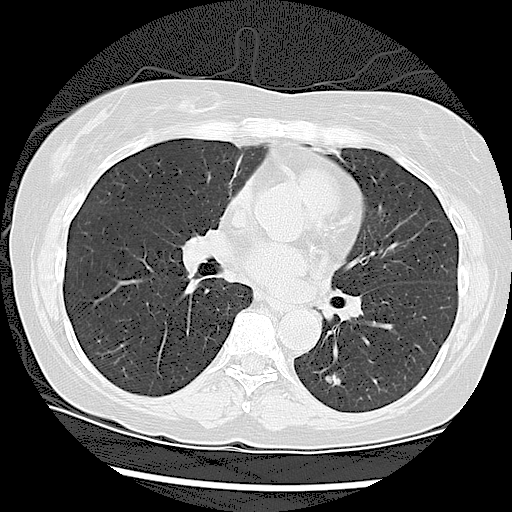
Low-dose screening chest CT, axial slice; second annual screen; lung window (W 1500 / L -600 HU); 2.5 mm slice thickness; slice 57 of 108 in the series; 512 × 512 image matrix. Female, age 61 years at enrolment. Current smoker at enrolment.
Expert-annotated lung lesion, bounding box <303,361,364,406> (left, top, right, bottom; pixels). The screening reader recorded 2 non-calcified nodules or masses ≥4 mm on this exam (left lower lobe, right lower lobe); which of them this box marks is not recorded. Official screen result: positive, other.